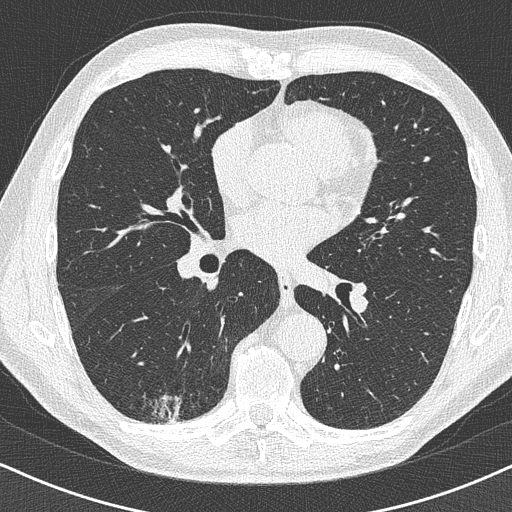
Chest CT (low-dose screening protocol), one axial image. Baseline annual screen. Lung window (W 1500 / L -600 HU). Lung (sharp) reconstruction kernel (B50f). Male, age 63 years at enrolment.
• Expert reader's lesion annotation, bounding box <130,362,202,428> (left, top, right, bottom; pixels).
• Reader record for this screening exam (exam-level; its link to the box is not recorded): non-calcified nodule or mass ≥4 mm, right lower lobe, 16 × 13 mm, poorly defined margins.
• Official screen result: positive, change unspecified: nodule(s) >= 4 mm or enlarging nodule(s), mass(es), or other non-specific abnormalities suspicious for lung cancer.
• Later outcome: lung cancer diagnosed 74 days after this screen — adenocarcinoma, NOS, right lower lobe, moderately differentiated (G2), stage IA (AJCC 6th edition), 20 mm at pathology.